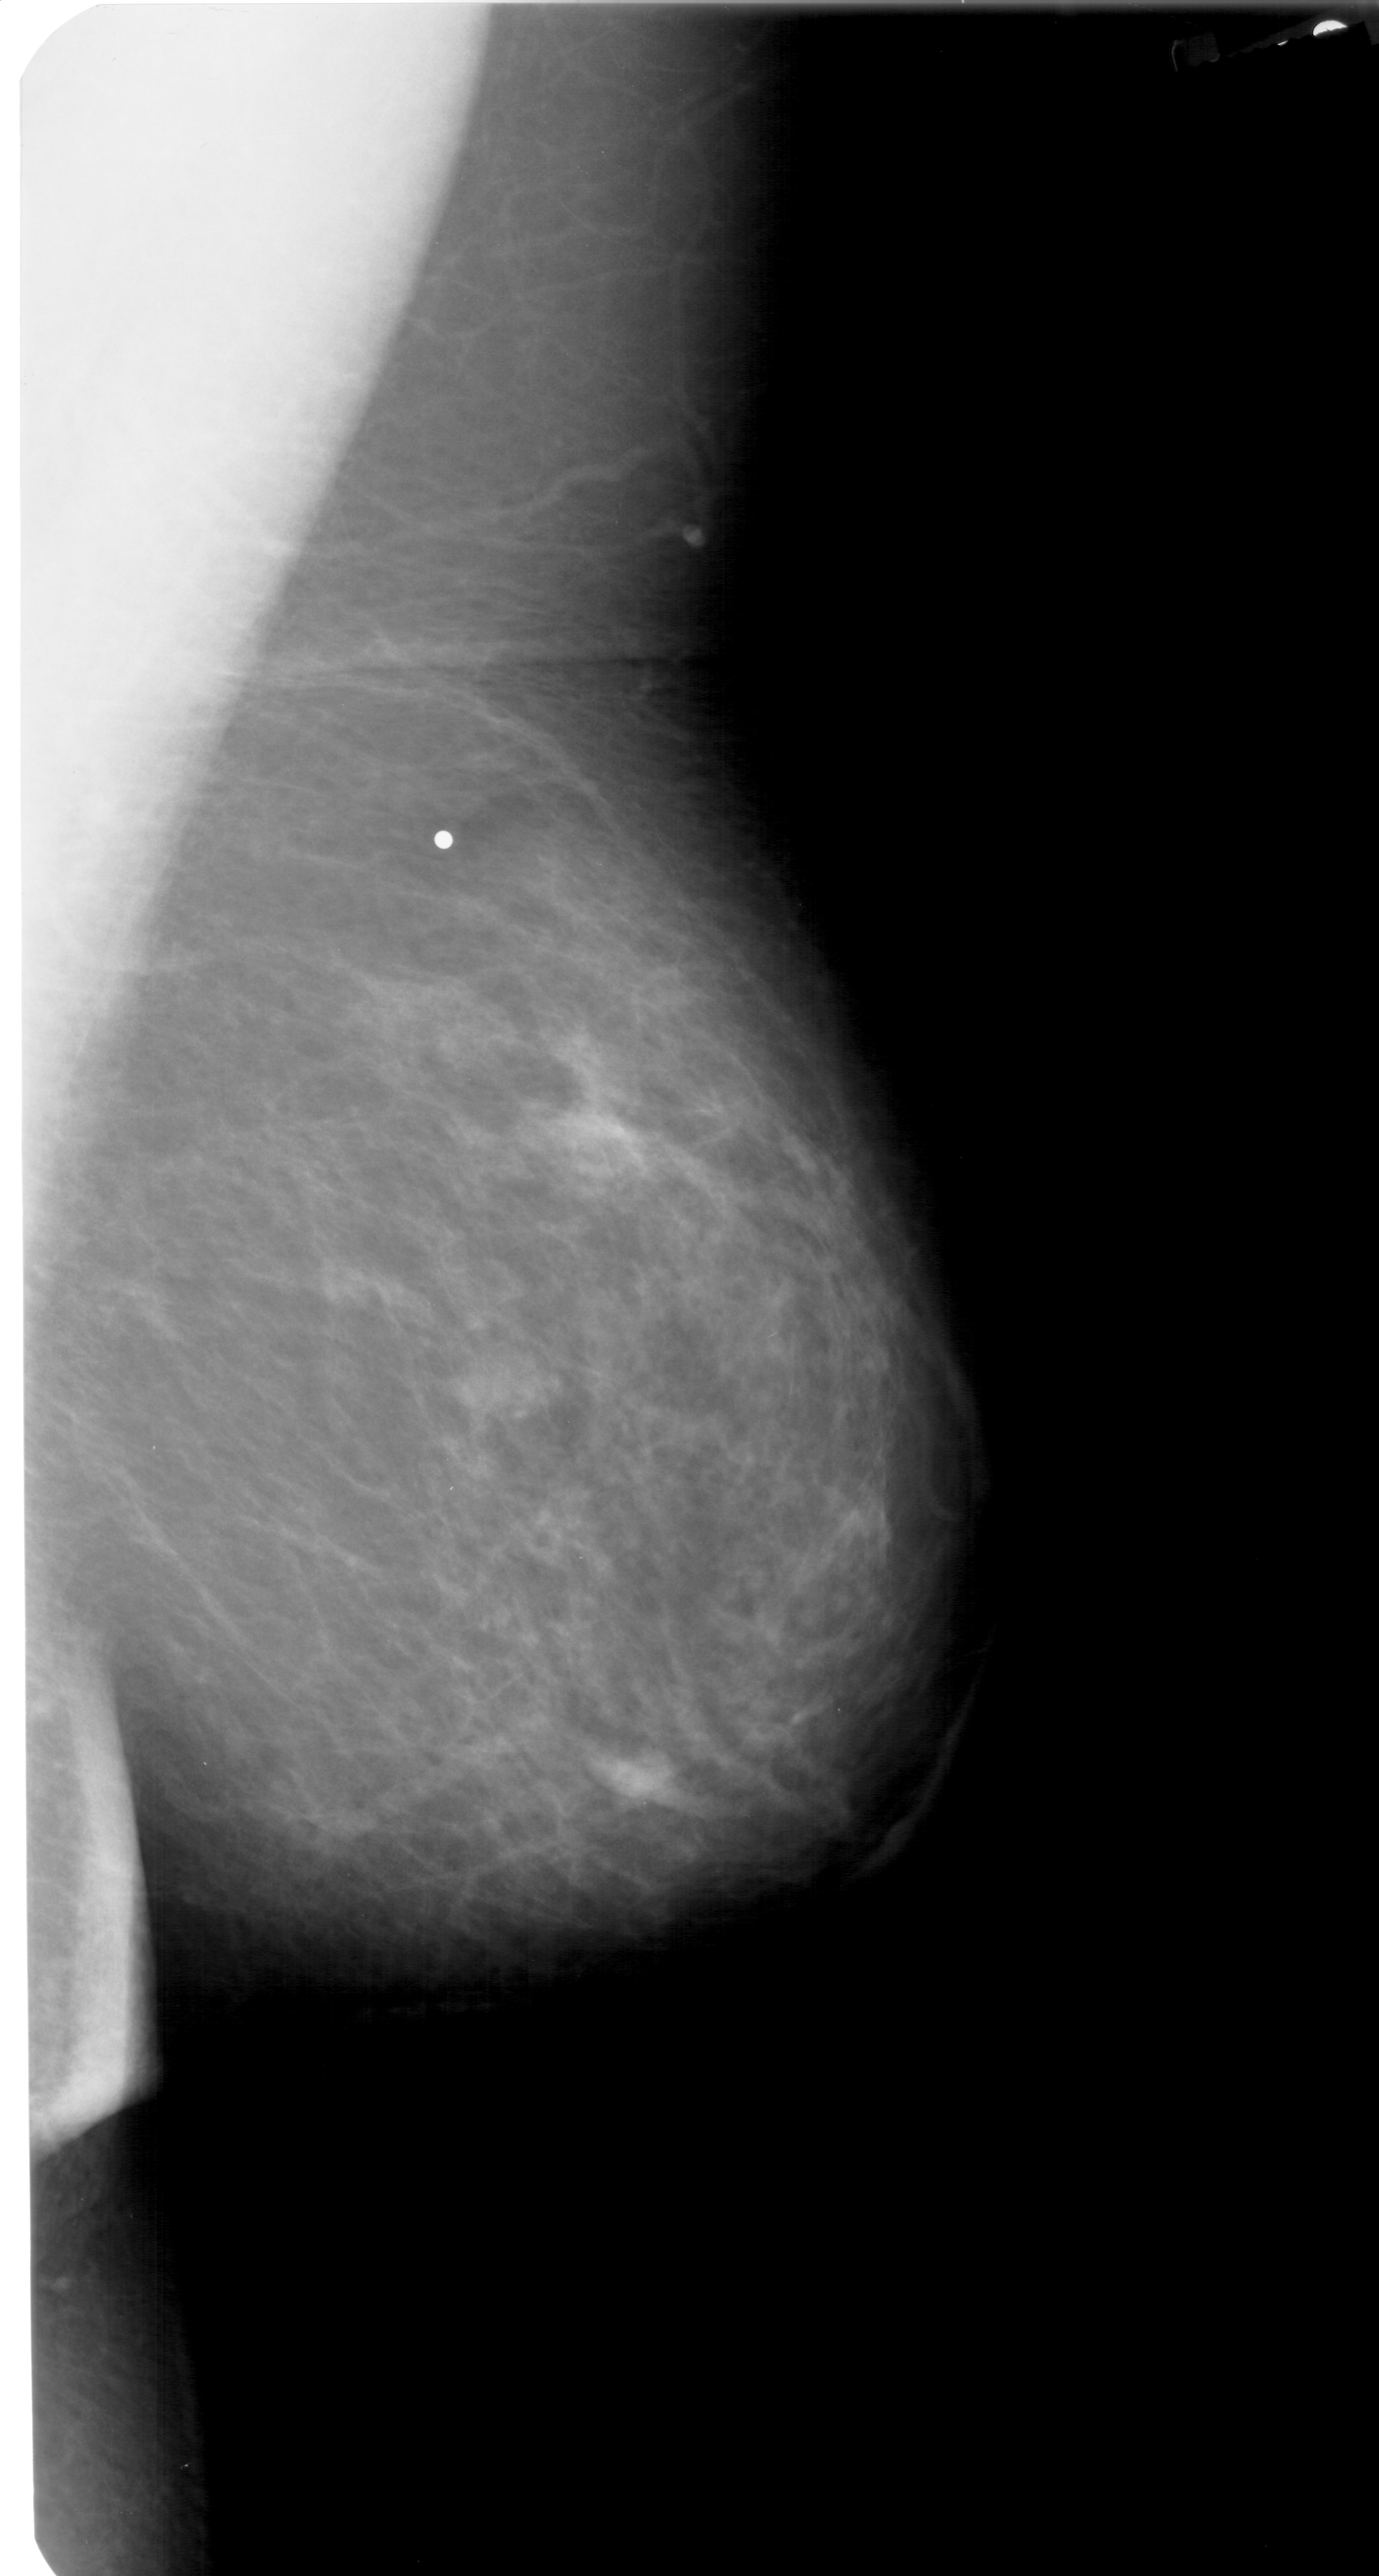
Digitized screen-film mammogram; right breast; MLO view; breast composition: scattered fibroglandular densities (BI-RADS density category 2 of 4); 1379 × 2576 image matrix.
Expert-marked regions of interest on this image (one box per marked abnormality):
- mass, shape oval, margins ill defined; BI-RADS assessment category 4; pathology (as recorded): benign: box from (x=434, y=1335) to (x=568, y=1445) px